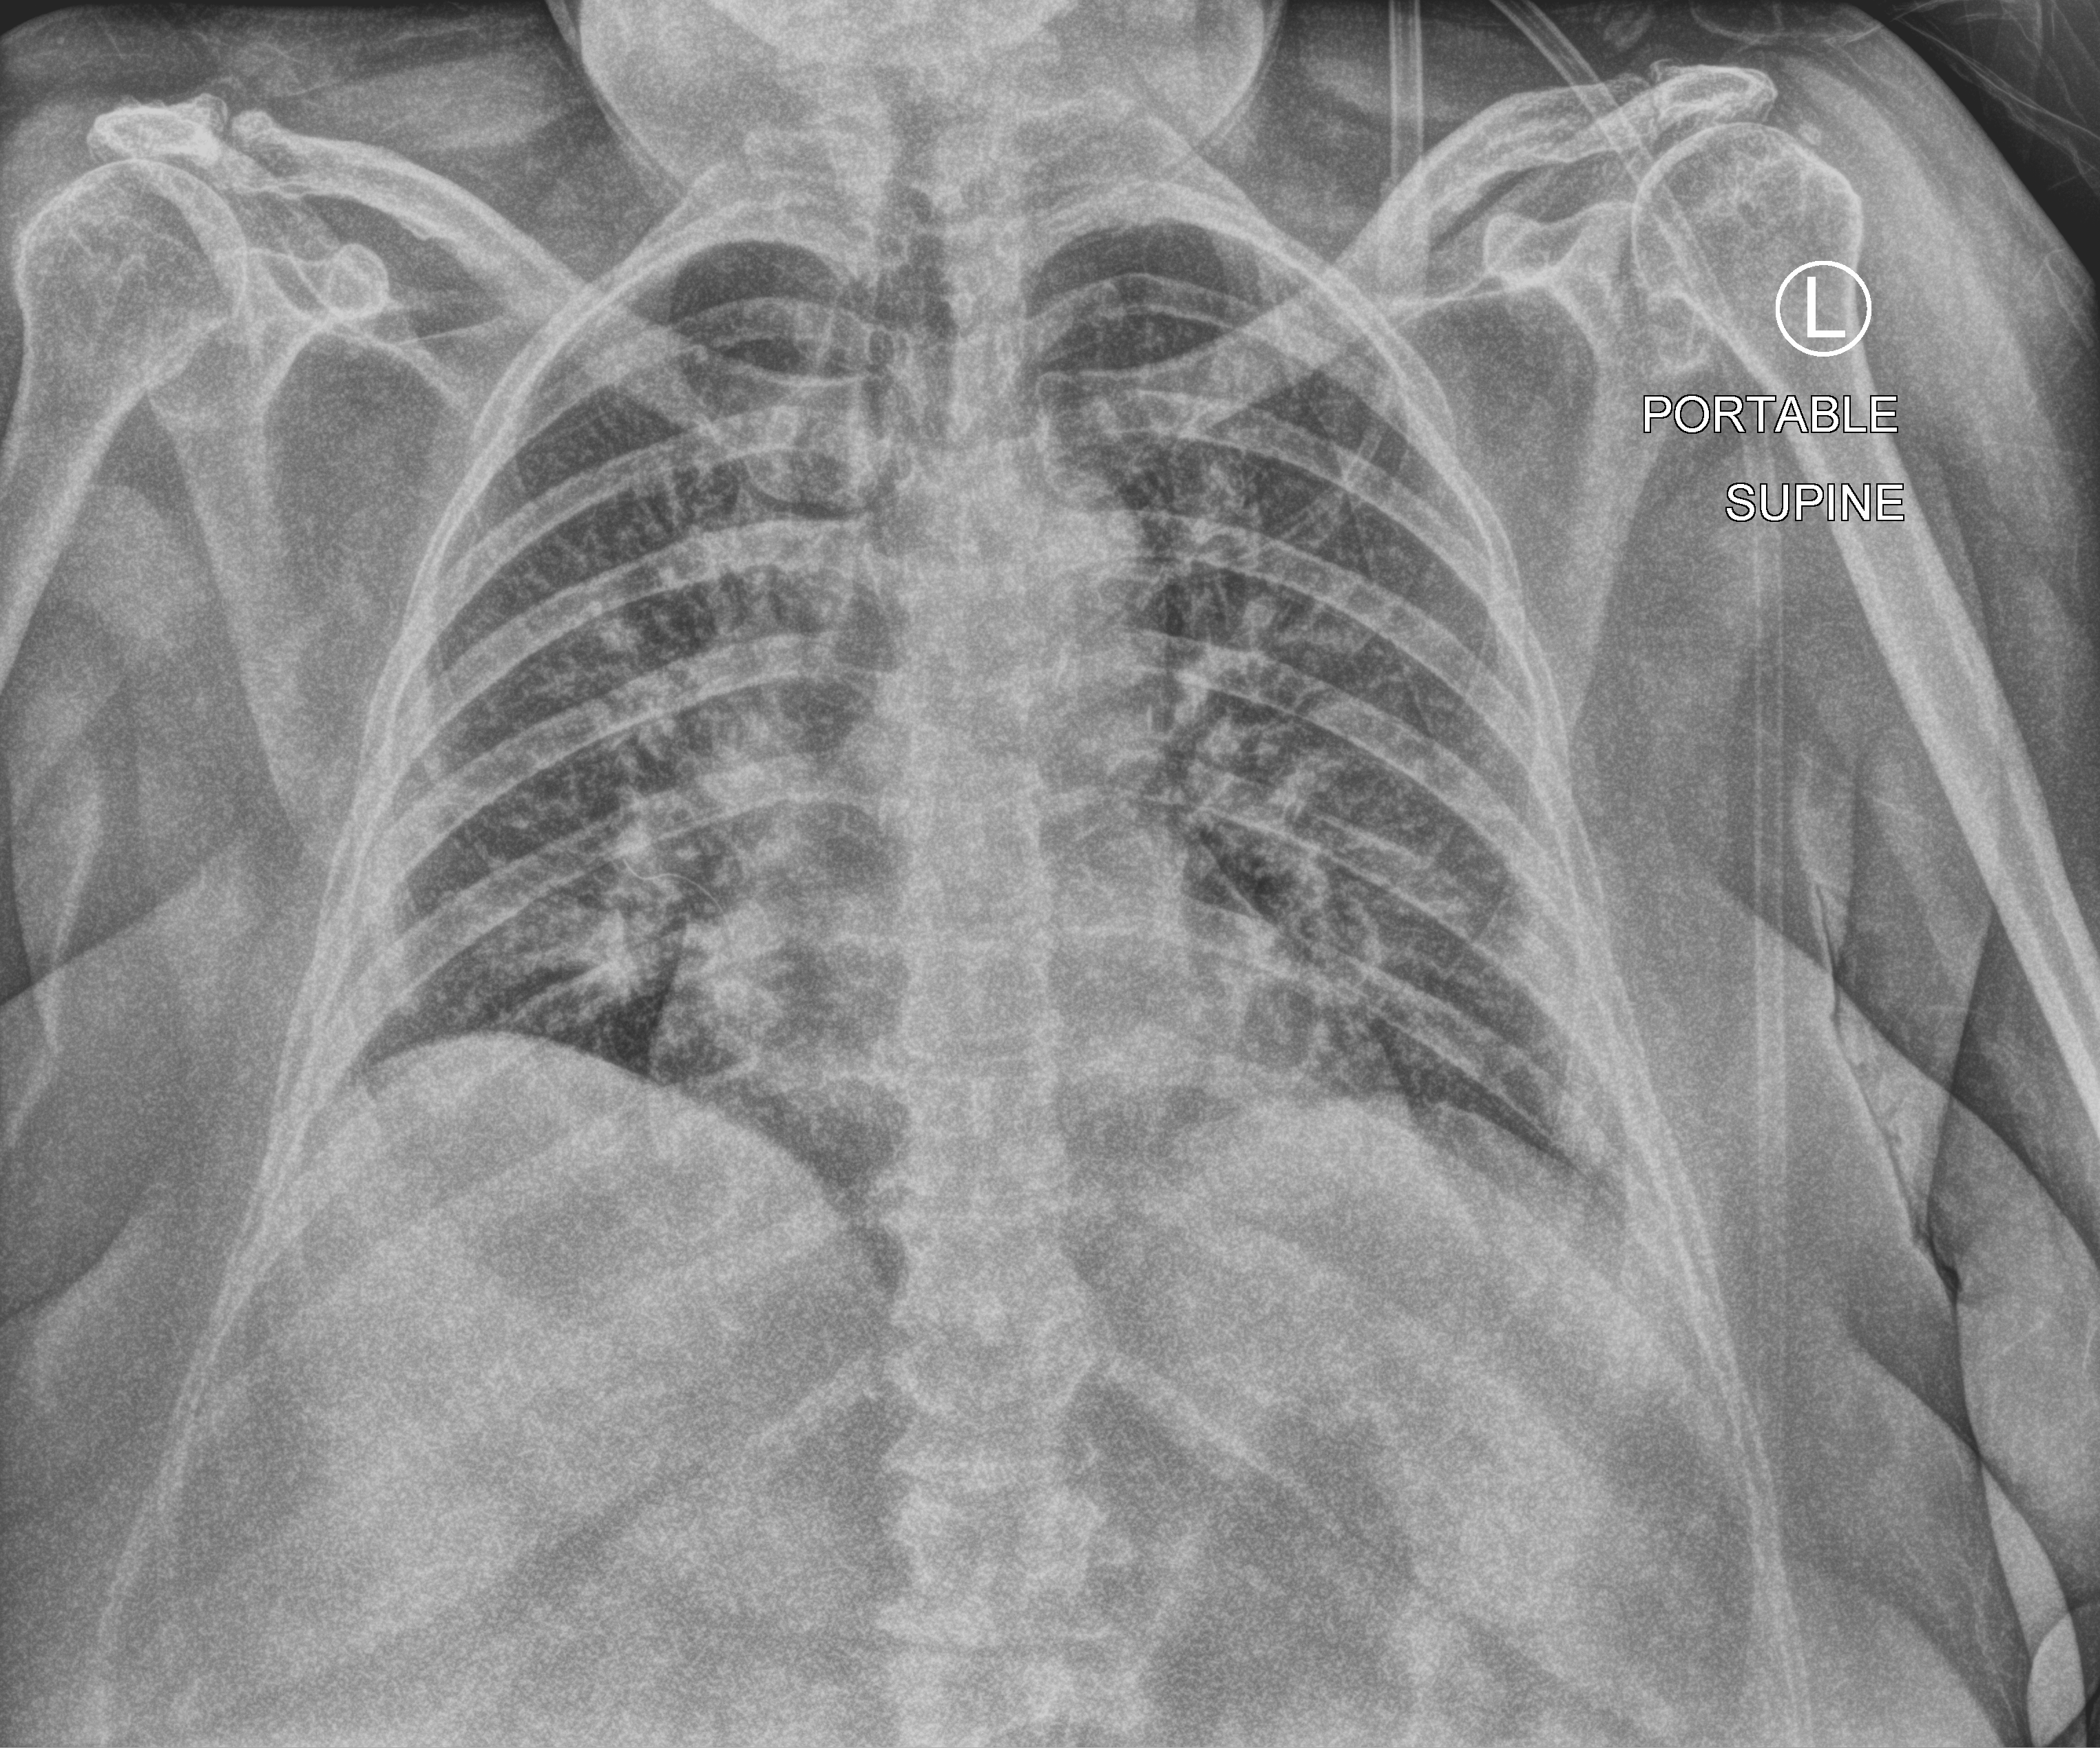
Chest X-ray (portable), anteroposterior (AP) projection. Patient hospitalised with COVID-19; female, aged 60–74 years.
From the hospital-stay record, not from the radiograph (when in the stay this image was taken is not recorded):
- length of hospital stay: 10 days